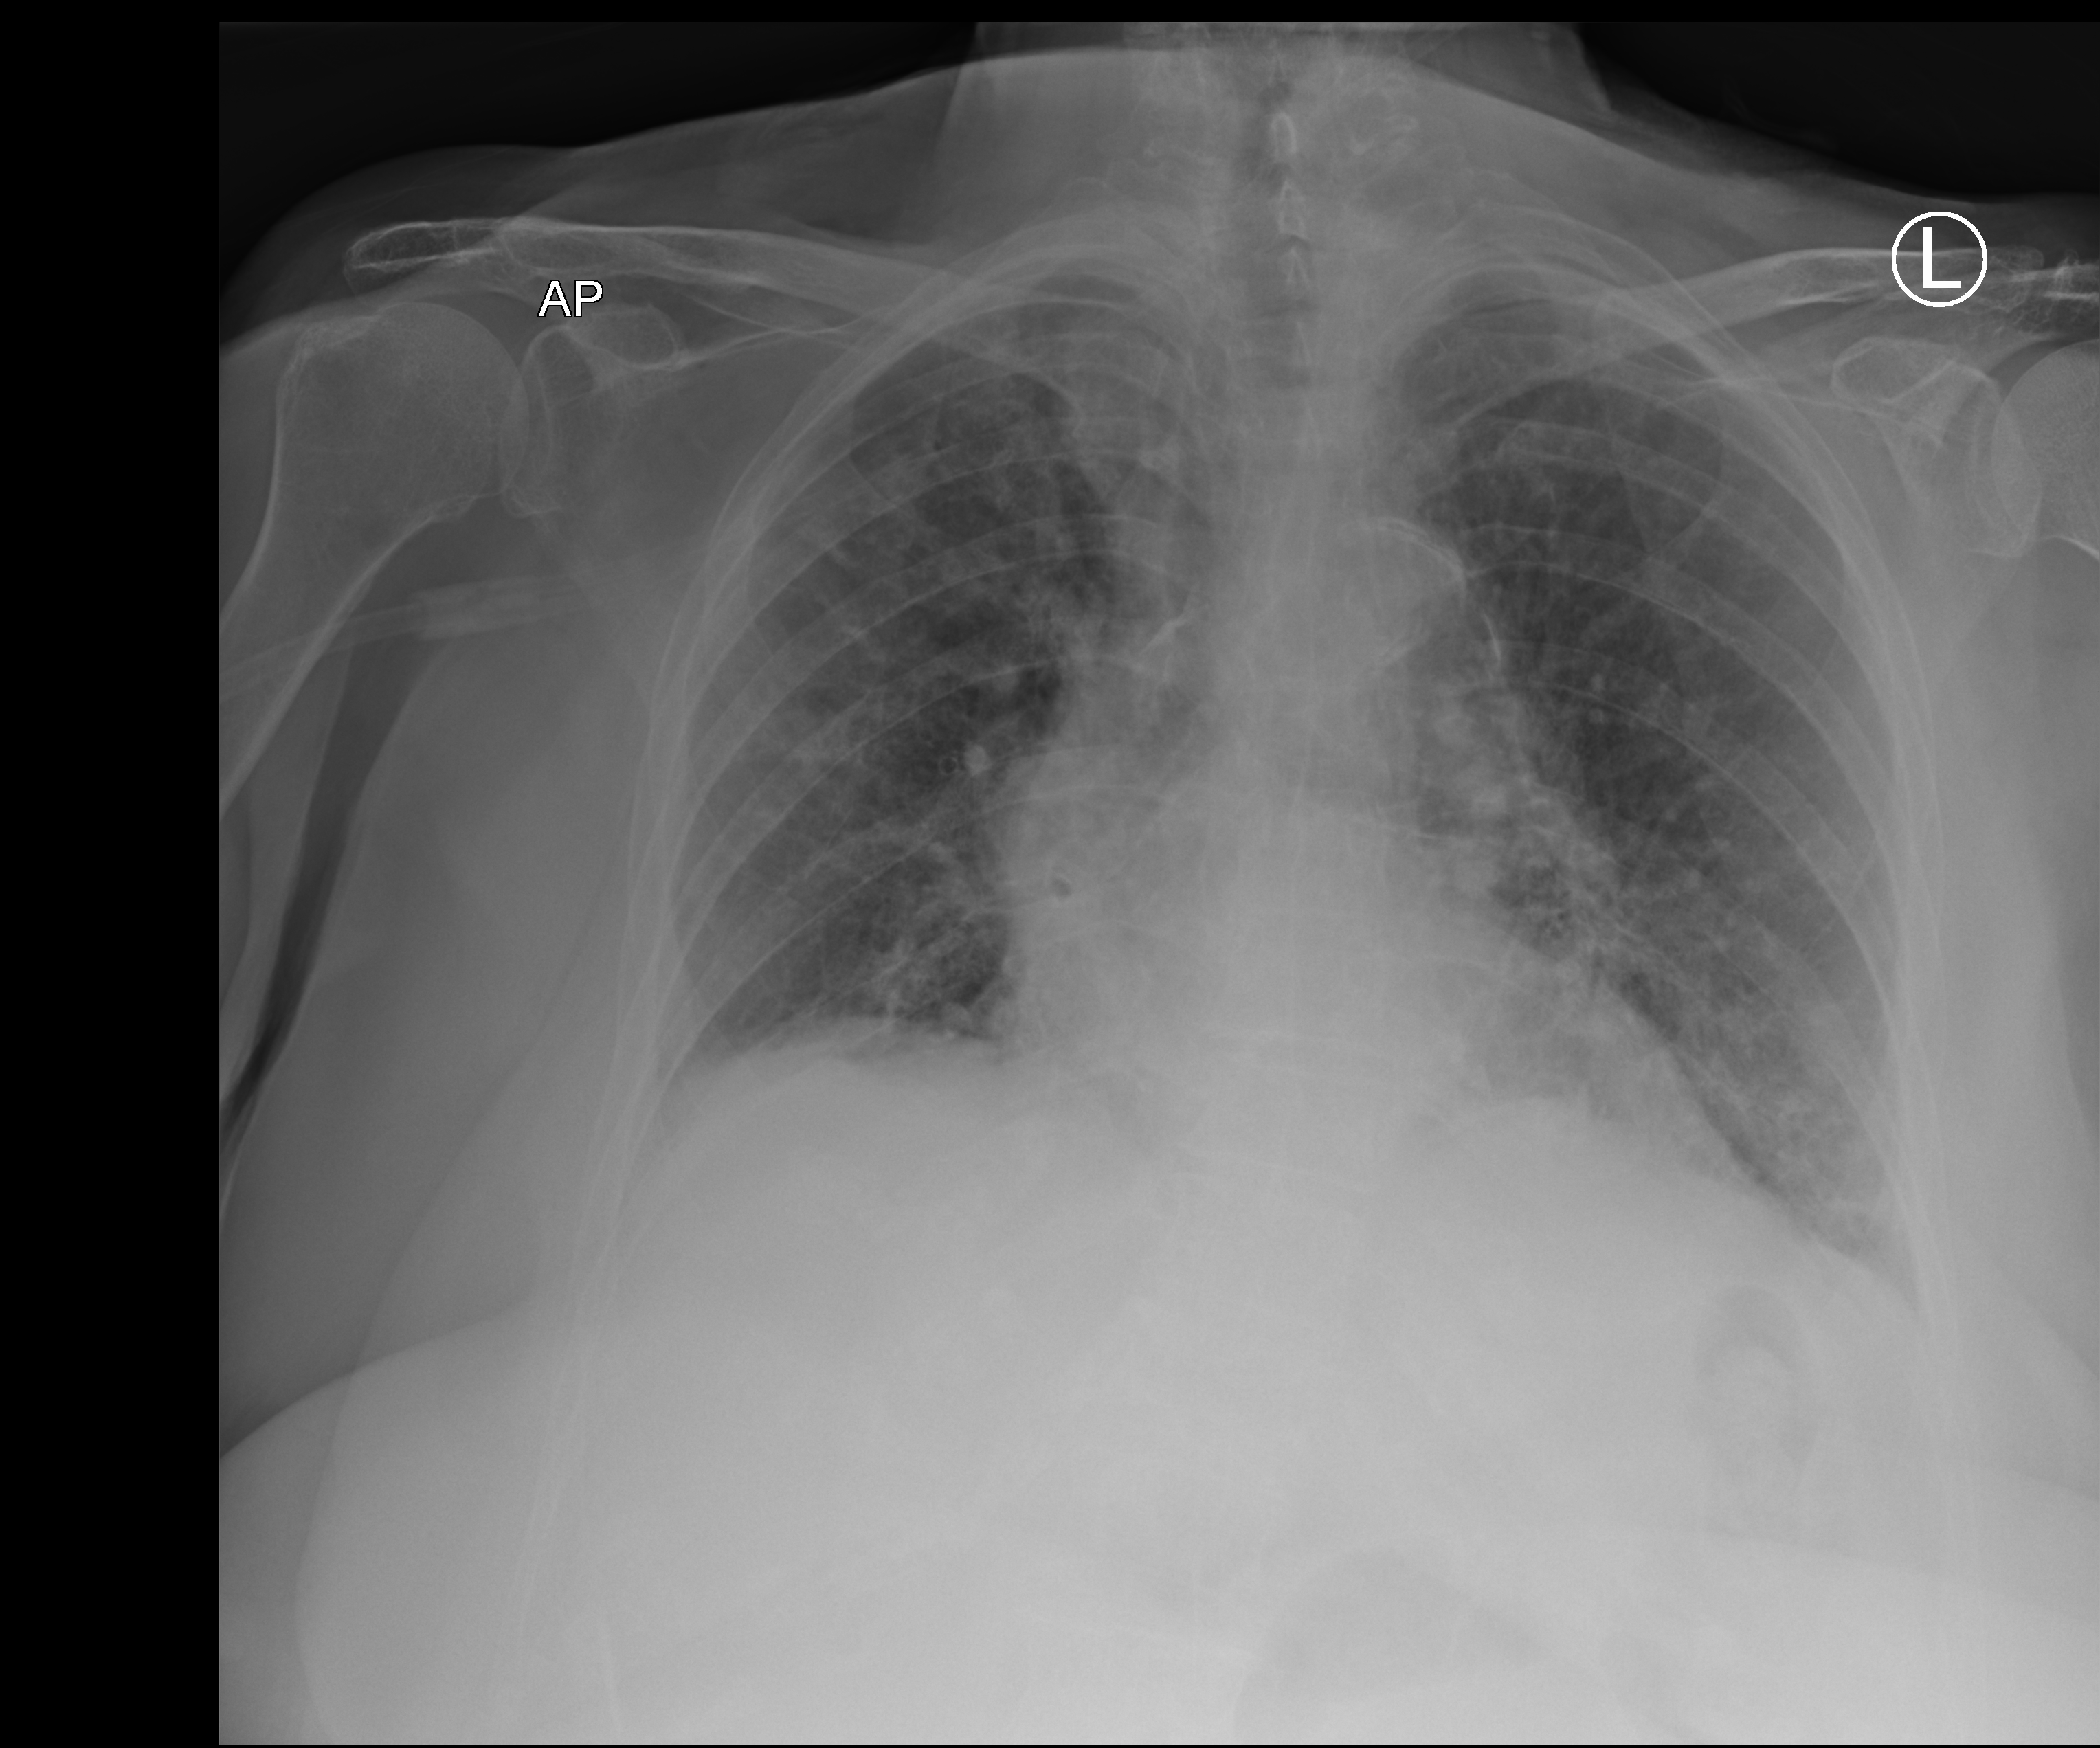
Bedside chest radiograph (computed radiography); anteroposterior (AP) projection. Female patient hospitalised with COVID-19, age 75–90 years.
Hospital-stay facts (about this admission, not read from this image; timing relative to this image not recorded): admitted to intensive care during this hospital stay: no.